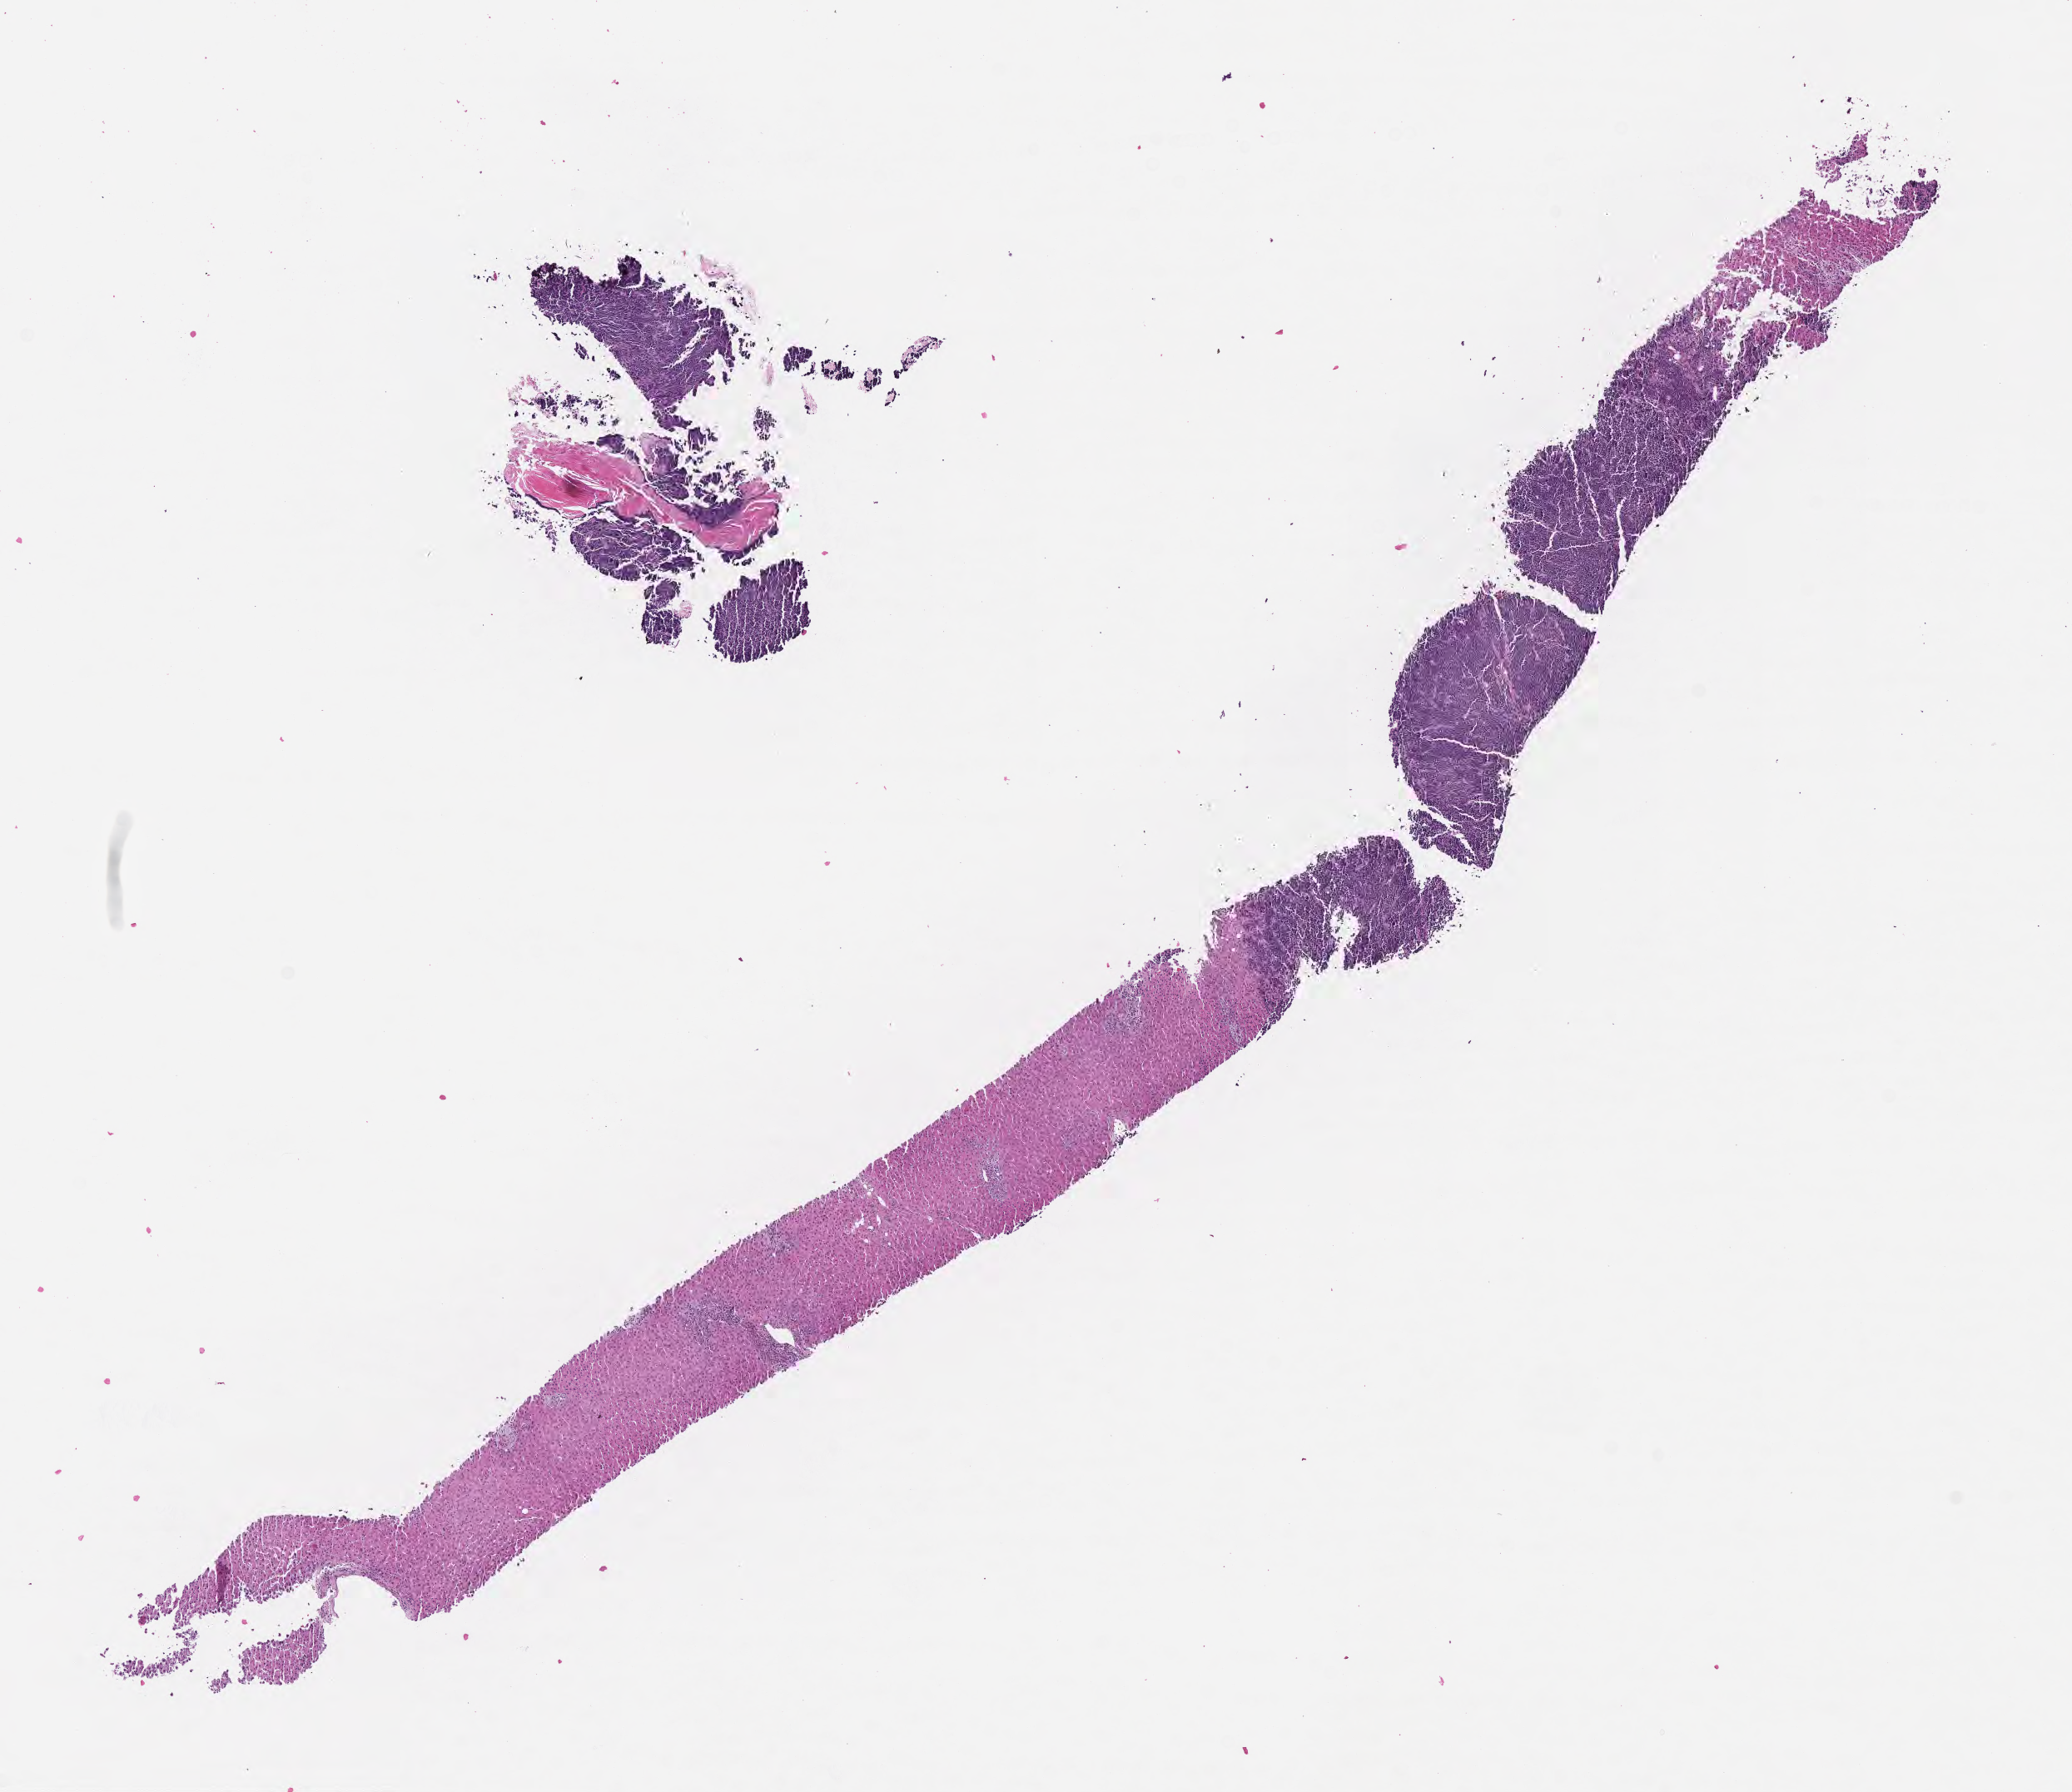
Whole-slide image, haematoxylin and eosin stain, whole scanned area (about 10.1 x 8.7 mm) shown as a low-resolution overview. FFPE section. Specimen: primary tumor. Male patient, aged 68. Composition of this section per pathologist review: tumor cells 35%, tumor nuclei 75%, stromal cells 10%, necrosis 5%, normal cells 50%. Inflammatory infiltration, as recorded: lymphocyte infiltration 50%, monocyte infiltration 10%, neutrophil infiltration 5%.
Ann Arbor stage (patient): Stage IV. Diagnosis: Burkitt lymphoma, NOS. Section: top of the tissue portion.